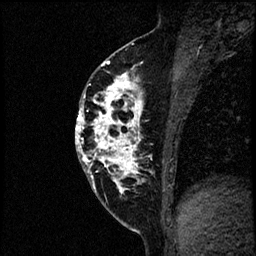
Breast MRI (dynamic contrast-enhanced), one sagittal slice; slice 31 of 60 in the series (ordered by position); dynamic contrast-enhanced study with each time point stored as its own series, time point 2 of 4 at this slice position (early post-contrast, ordered by acquisition time); 1.5 T; TE 4.2 ms, TR 17.6 ms; 2 mm slice thickness; 256 × 256 image matrix. Patient: female, 40 years. From the clinical record (not read from this slice): setting: breast cancer imaged before/during neoadjuvant chemotherapy; receptor status: HER2-positive.
Outlined on this slice (semi-automatic segmentation, software-assisted and operator-edited):
- analysis volume of interest (the breast-tissue region the enhancement analysis was run in; not a lesion): bounding box [x1, y1, x2, y2] px = [76, 56, 197, 205]
- tumour enhancement mask (voxels above the 100 % enhancement threshold inside the analysis volume of interest): [77, 60, 145, 190]